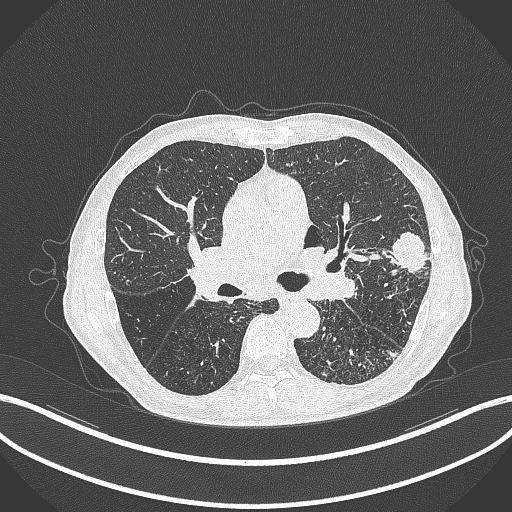
Chest CT, one axial slice. Slice 242 of 463 in the series (ordered by position). 120 kVp. Lung window (W 1500 / L -600 HU). 512 × 512 image matrix, field of view 400 × 400 mm. Male patient, age 74 years. From the clinical record (not read from this slice): clinical TNM (as recorded): T2a N1 M0.
Structures marked on this image (rectangle marked by the reading radiologist):
- lung tumour (recorded histology: adenocarcinoma): bounding box [x1, y1, x2, y2] px = [383, 225, 427, 278]